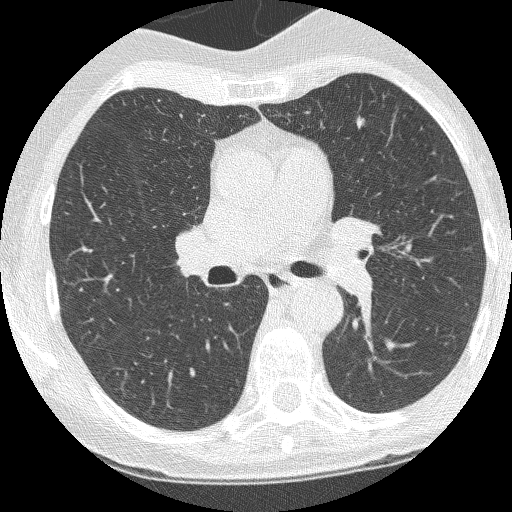
Low-dose screening chest CT, axial slice; third screening round (two years after baseline); lung window (W 1500 / L -600 HU); 1.25 mm slice thickness; slice 158 of 247 in the series; 512 × 512 image matrix. Female participant, aged 60 years at enrolment. Current smoker at enrolment.
Expert-annotated lung lesion, bounding box (x1, y1, x2, y2) in pixels: (346, 110, 375, 142). The screening reader recorded 2 non-calcified nodules or masses ≥4 mm on this exam (left upper lobe, left upper lobe); which of them this box marks is not recorded. Lung cancer was diagnosed 37 days after this screen: adenocarcinoma, NOS, left upper lobe, moderately differentiated (G2), stage IA (AJCC 6th edition), 6 mm at pathology.